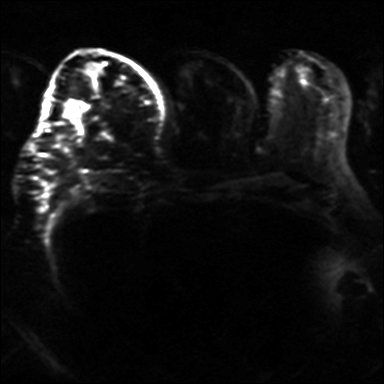
Breast MRI, one axial slice. Slice 18 of 36 in the series (ordered by position). Diffusion-weighted series; image 2 of 4 stored at this slice position (different b-values; order by instance number). 3 T. 384 × 384 image matrix. Female patient.
Structures marked on this image (expert manual segmentation):
- tumour on diffusion-weighted imaging: box from (x=63, y=102) to (x=84, y=133) px